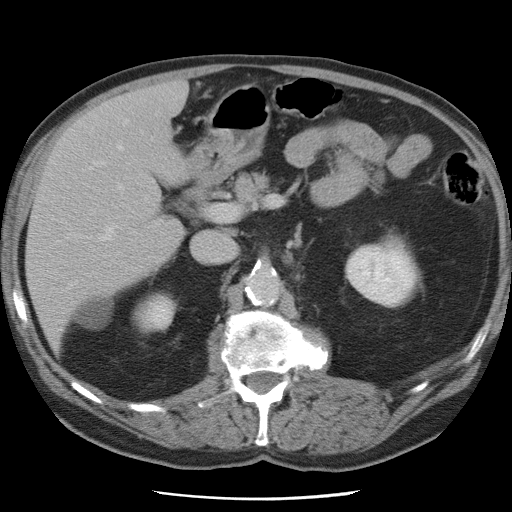
Contrast-enhanced abdominal CT, one axial slice. Slice 40 of 78 in the series (ordered by position). 120 kVp. Soft-tissue window (W 400 / L 40 HU). 5 mm slice thickness. 512 × 512 image matrix, field of view 337 × 337 mm. Male patient, age 75 years. From the clinical record (not read from this slice): diagnosis: colorectal cancer liver metastases, imaged before liver resection; multiple liver metastases: yes; largest metastasis: 2.4 cm; disease in both lobes: yes.
Outlined on this slice (manually delineated by an expert):
- hepatic veins: bounding box [x1, y1, x2, y2] px = [95, 121, 127, 241]
- liver: [28, 83, 187, 344]
- planned liver remnant (the part of the liver to remain after resection): [28, 119, 182, 343]
- portal vein (with intrahepatic branches): [117, 185, 121, 188]